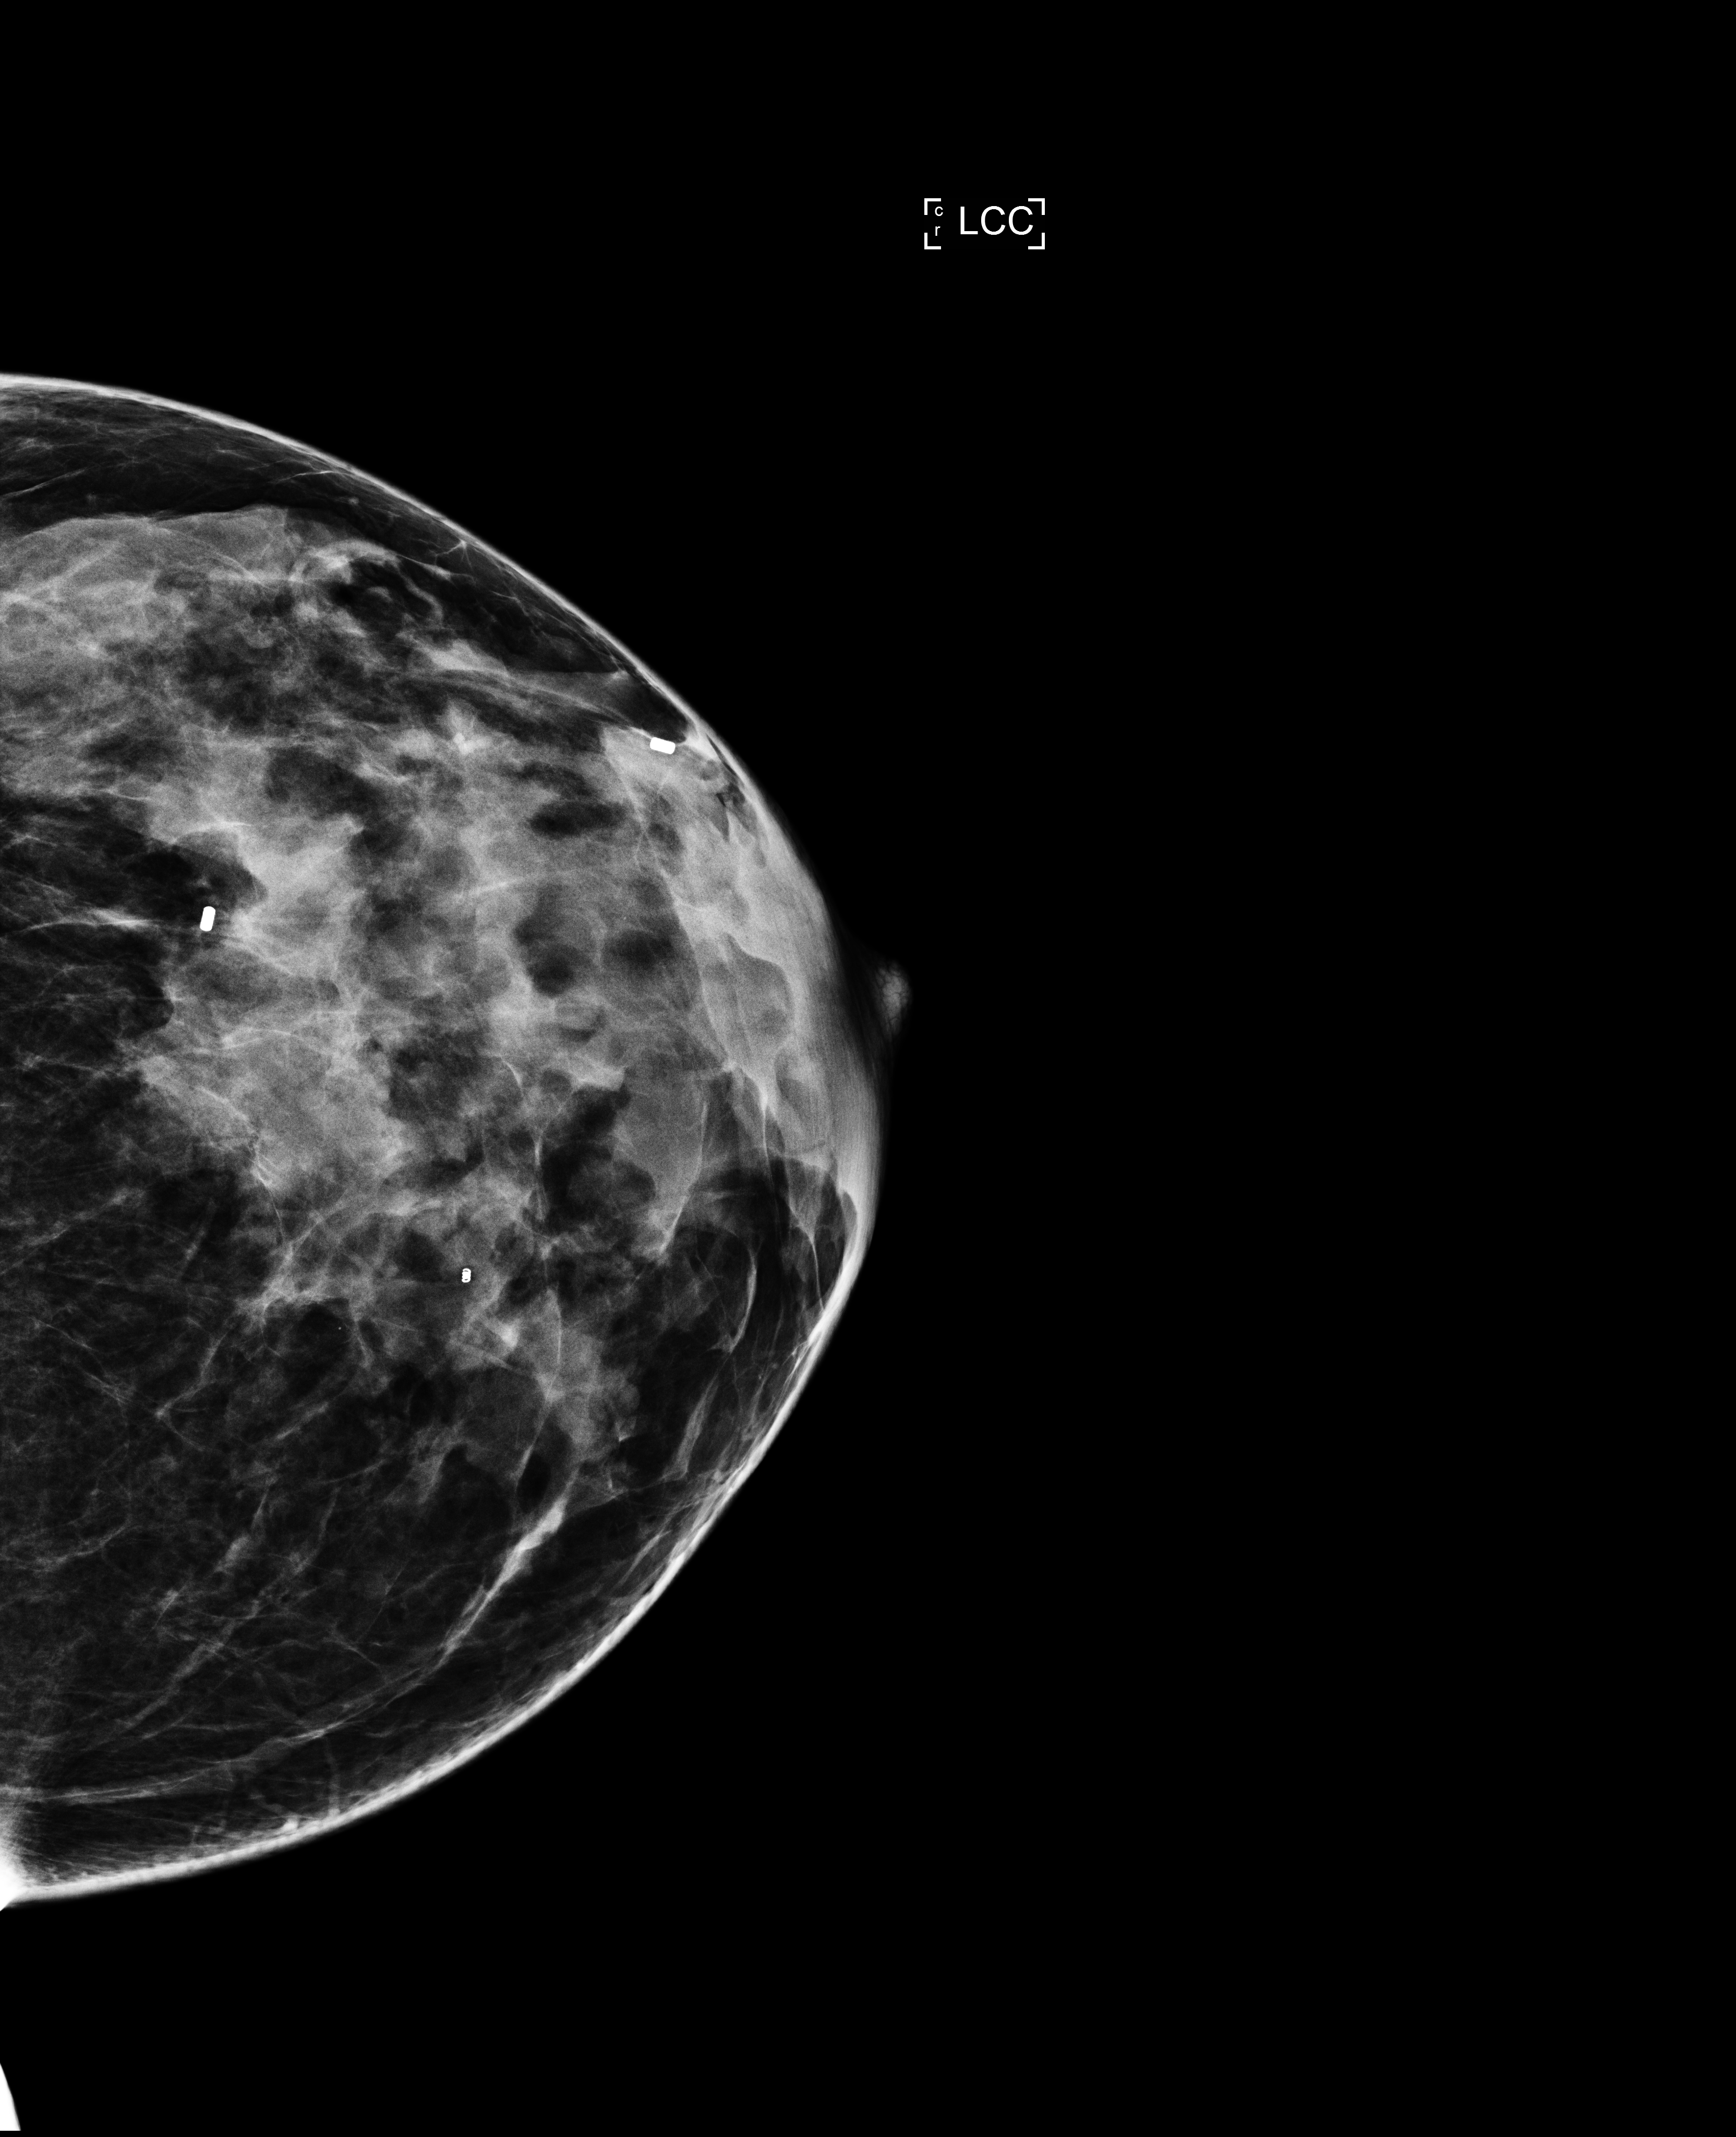
Screening examination. Patient aged 49 years (female).
Image type: full-field digital mammogram. Breast: left. Projection: CC view.